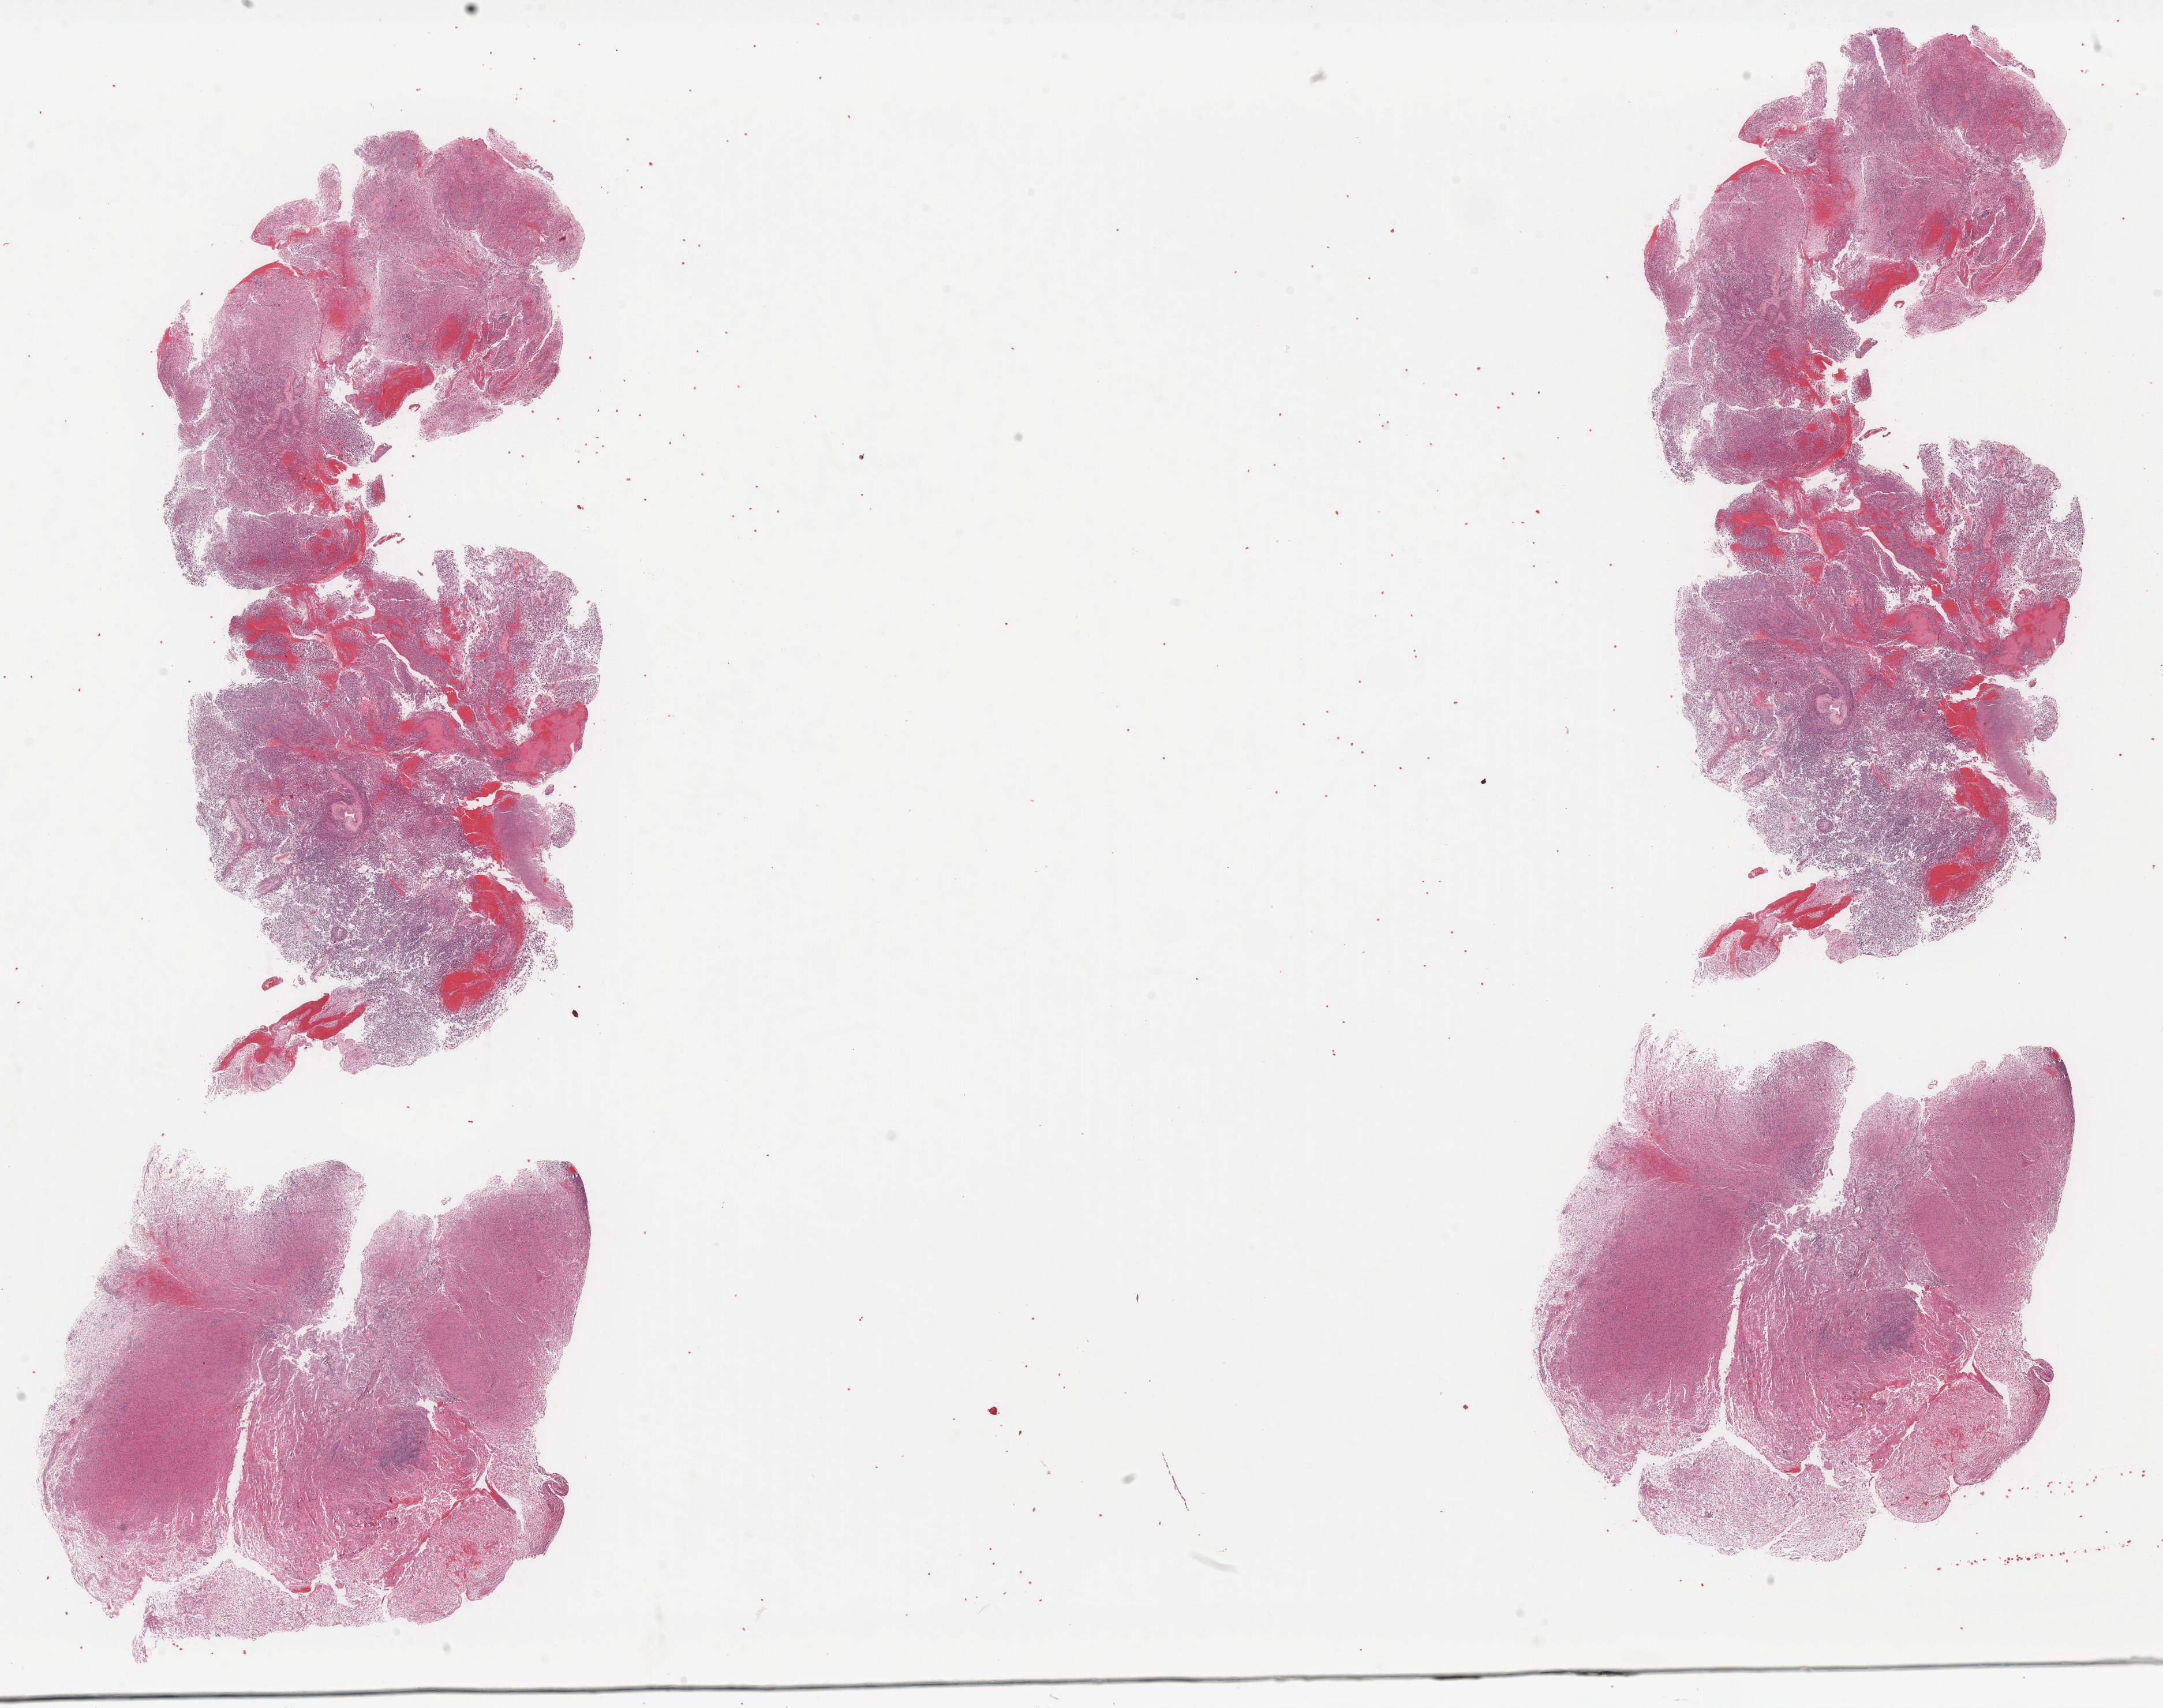
Digitized H&E tissue section (whole slide), low-resolution overview of the scanned area, about 29.7 x 23.4 mm (acquisition: 40x scan). Formalin-fixed paraffin-embedded (FFPE) diagnostic section. Primary tumour sample from the brain. Male patient; age at initial diagnosis 68 years.
• diagnosis: Glioblastoma (temporal lobe)